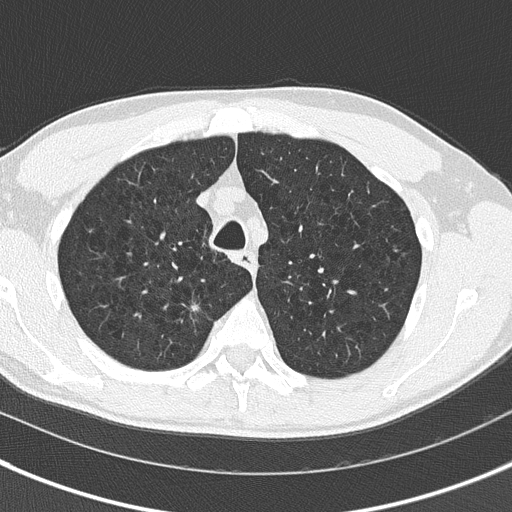
Axial slice from a low-dose chest CT screening exam. Baseline annual screen. Lung window (W 1500 / L -600 HU). 2 mm slice thickness. Slice 41 of 175 in the series. 512 × 512 image matrix. Male participant, aged 56 years at enrolment.
Lesion marked by an expert reader, bounding box (x1, y1, x2, y2) in pixels: (177, 293, 225, 335). The screening reader recorded 3 non-calcified nodules or masses ≥4 mm on this exam (right upper lobe, right upper lobe, left lower lobe); which of them this box marks is not recorded. Later outcome: lung cancer diagnosed 228 days after this screen — non-small cell carcinoma, right upper lobe, stage IIIA (AJCC 6th edition), 21 mm at pathology.